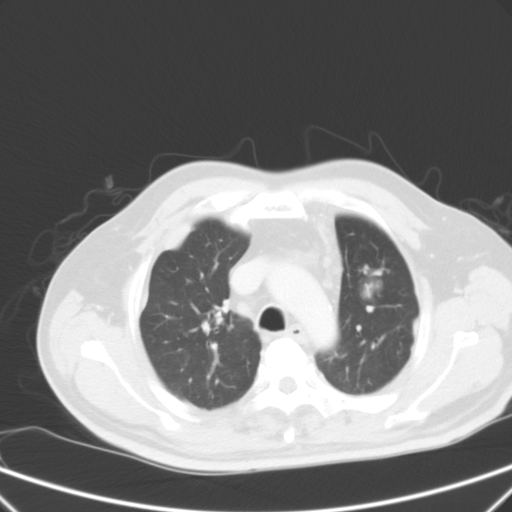
Chest CT, one axial slice. Position 44 of 59 along the scan axis. Intravenous contrast given. Lung window (W 1500 / L -600 HU). 512 × 512 image matrix, field of view 357 × 357 mm. Patient: male, 66 years. Case-level facts recorded for this patient, not image findings: clinical TNM (as recorded): T1c N3 M1a.
Outlined on this slice (rectangle marked by the reading radiologist):
- lung tumour (recorded histology: squamous cell carcinoma): bounding box [x1, y1, x2, y2] px = [355, 264, 392, 304]